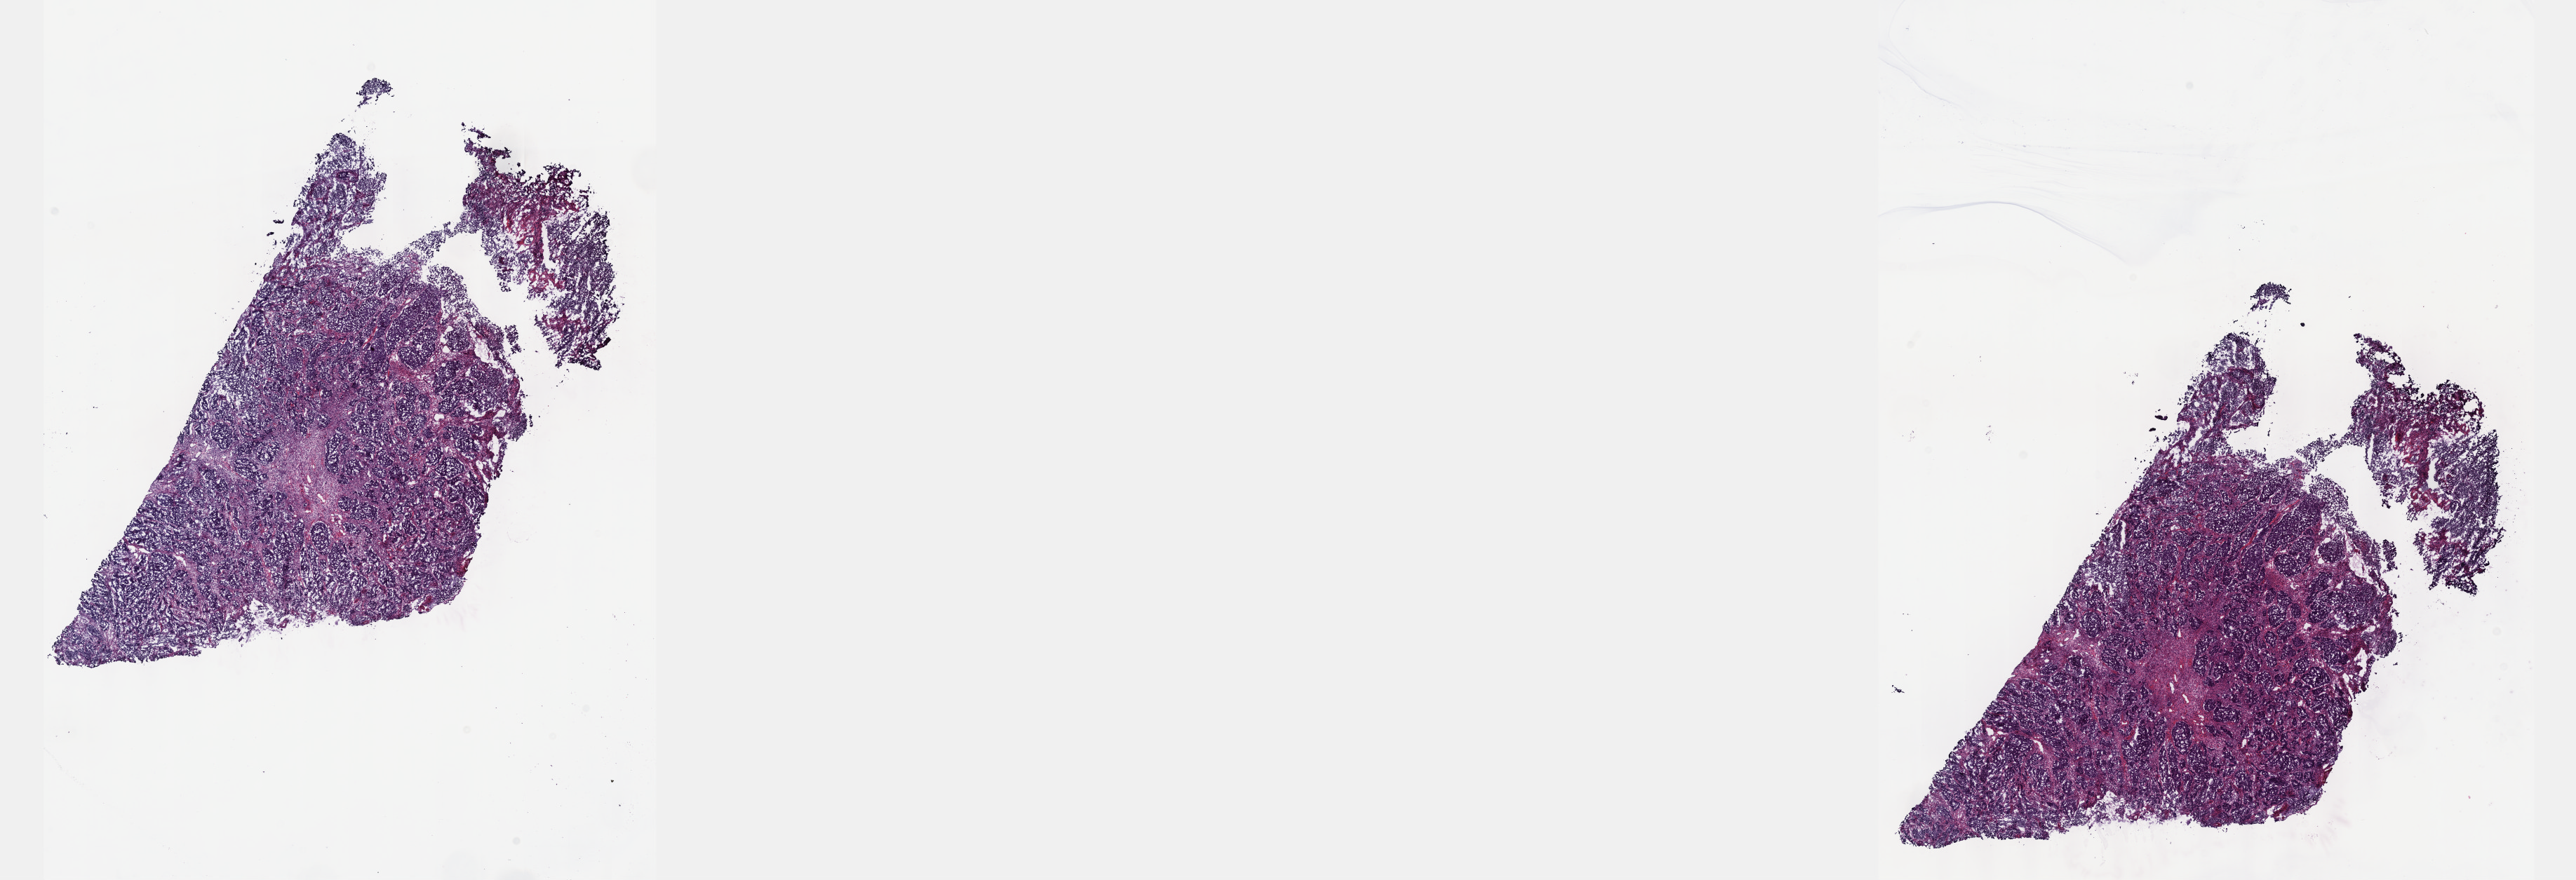
Digitized H&E-stained tissue section (whole slide), low-resolution overview of the scanned area, about 29.7 x 10.1 mm; frozen section from the top of the tissue portion; primary tumour sample from the cervix. Female, age 42 years at initial diagnosis. Histologic grade: G3 (poorly differentiated). Composition of this section per pathologist review: tumour cells 75%, tumour nuclei 85%, normal cells 0%, stromal cells 25%, necrosis 0%. Inflammatory infiltration, as recorded: lymphocyte infiltration 0%, monocyte infiltration 0%, neutrophil infiltration 0%.
• histologic diagnosis: Adenocarcinoma, endocervical type (cervix uteri)
• FIGO stage: IB2